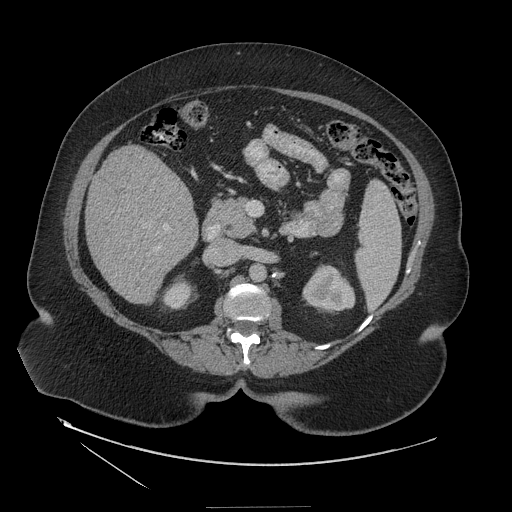
Contrast-enhanced abdominal CT (liver protocol), one axial slice. Slice 57 of 127 in the series (ordered by position). Reconstruction kernel STANDARD. Soft-tissue window (W 400 / L 40 HU). 512 × 512 image matrix. From the clinical record (not read from this slice): diagnosis: hepatocellular carcinoma (patient treated with transarterial chemoembolisation; whether this scan precedes or follows treatment is not stated here); TNM stage (as recorded): Stage-II; Child-Pugh class: A; tumour differentiation: well differentiated; tumour nodularity: multinodular.
Structures marked on this image (semi-automatically segmented with operator editing):
- liver parenchyma outside the tumour (the mass and vessels are separate outlines, so this box may not span the whole liver): bounding box (x1, y1, x2, y2) in pixels: (86, 146, 198, 304)